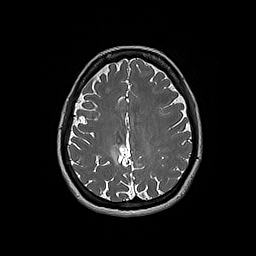
Brain MRI from a brain-tumour surgery series, one axial slice. Slice 68 of 192 in the series (ordered by position). 1 mm slice thickness. 256 × 256 image matrix, field of view 250 × 250 mm. From the clinical record (not read from this slice): histopathology: Oligodendroglioma; WHO grade: 2; IDH mutation: yes; tumour location: Right Parietal.
Annotated regions visible in this slice (expert manual segmentation):
- tumour: bounding box <110,143,125,165> (left, top, right, bottom; pixels)